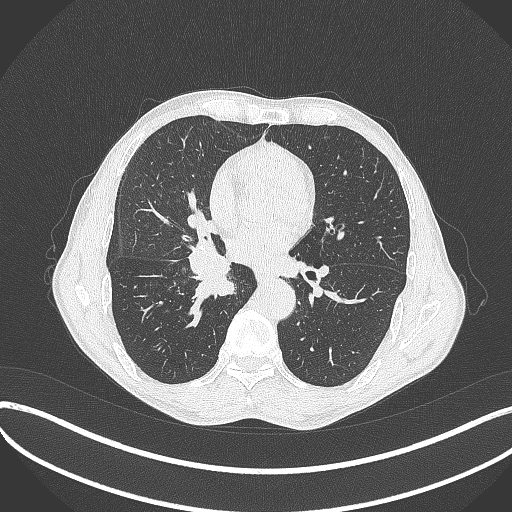
Chest CT, one axial slice. Slice 206 of 481 in the series (ordered by position). Reconstruction kernel B70f. Lung window (W 1500 / L -600 HU). 512 × 512 image matrix, field of view 400 × 400 mm. Male patient, age 65 years. From the clinical record (not read from this slice): clinical TNM (as recorded): T2a N0 M0; histopathological grade: G2.
Outlined on this slice (bounding box drawn by a radiologist):
- lung tumour (recorded histology: squamous cell carcinoma): box from (x=182, y=240) to (x=237, y=300) px